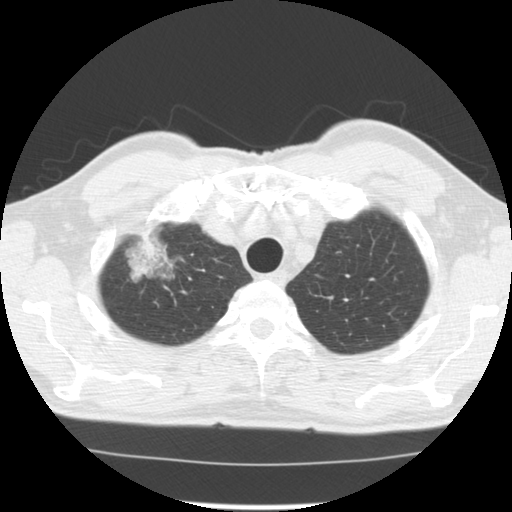
Axial slice from a low-dose chest CT screening exam, third screening round (two years after baseline), lung window (W 1500 / L -600 HU), 512 × 512 image matrix. Male participant, aged 64 years at enrolment. Former smoker at enrolment.
Expert-annotated lung lesion, bounding box (x1, y1, x2, y2) in pixels: (122, 232, 193, 292). The screening reader recorded 3 non-calcified nodules or masses ≥4 mm on this exam (right upper lobe, right lower lobe, left upper lobe); which of them this box marks is not recorded. Official screen result: positive, other. Later outcome: lung cancer diagnosed 30 days after this screen — adenocarcinoma, NOS, right upper lobe, well differentiated (G1), stage IB (AJCC 6th edition), 45 mm at pathology.